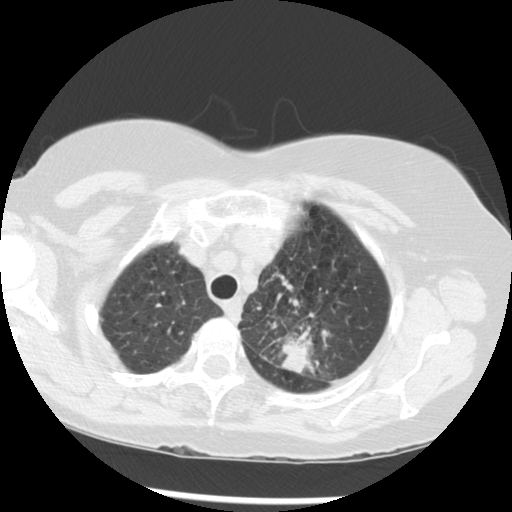
Low-dose screening chest CT, axial slice; third screening round (two years after baseline); lung window (W 1500 / L -600 HU); 2.5 mm slice thickness; slice 237 of 283 in the series. Female, age 70 years at enrolment. Current smoker at enrolment.
Expert reader's lesion annotation, bounding box (x1, y1, x2, y2) in pixels: (251, 286, 349, 374). Reader record for this screening exam (exam-level; its link to the box is not recorded): non-calcified nodule or mass ≥4 mm, left upper lobe, 32 × 26 mm, spiculated (stellate) margins, soft tissue attenuation, pre-existing on the prior screen: yes; interval growth: yes. Later outcome: lung cancer diagnosed 24 days after this screen — neoplasm, malignant, left upper lobe, stage IIIB (AJCC 6th edition), 40 mm at pathology.